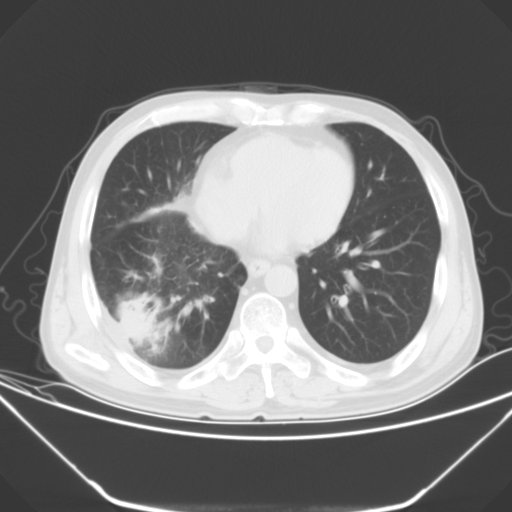
Chest CT, one axial slice. 120 kVp. Lung window (W 1500 / L -600 HU). 5 mm slice thickness. 512 × 512 image matrix, field of view 379 × 379 mm. Male patient, age 54 years. Case-level facts recorded for this patient, not image findings: clinical TNM (as recorded): T2 N1 M0.
Structures marked on this image (bounding box drawn by a radiologist):
- lung tumour (recorded histology: adenocarcinoma): bounding box (x1, y1, x2, y2) in pixels: (119, 293, 158, 343)